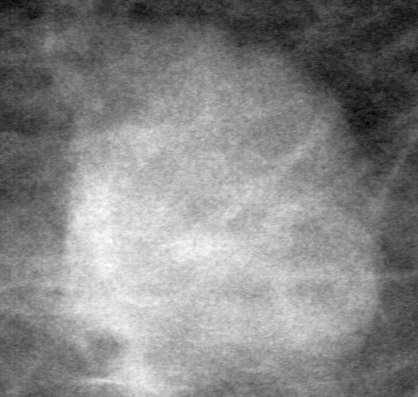
Cropped region of a digitized screen-film mammogram centred on a radiologist-marked abnormality, left breast, MLO view, BI-RADS breast density category 1 (scale 1–4).
Marked abnormality: mass, shape lobulated, margins circumscribed; BI-RADS assessment category 0; subtlety rating 5 on a 1 (subtle) to 5 (obvious) scale; pathology result (as recorded, not read from the image): benign.